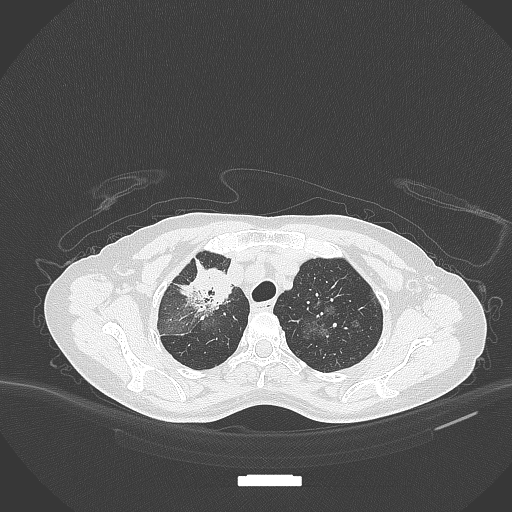
Chest CT, one axial slice; slice 264 of 284 in the series (ordered by position); reconstruction kernel B70f; 120 kVp; lung window (W 1500 / L -600 HU); 512 × 512 image matrix, field of view 400 × 400 mm. Patient: female, 59 years. From the clinical record (not read from this slice): clinical TNM (as recorded): T3 N0 M0.
Outlined on this slice (rectangle marked by the reading radiologist):
- lung tumour (recorded histology: adenocarcinoma): bounding box [x1, y1, x2, y2] px = [179, 266, 234, 316]